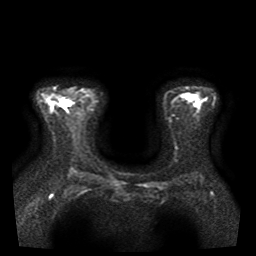
Breast MRI, one axial slice. Position 29 of 41 along the scan axis. Diffusion-weighted series; image 2 of 4 stored at this slice position (different b-values; order by instance number). 1.5 T. 5 mm slice thickness. 256 × 256 image matrix, field of view 330 × 330 mm. Female patient.
Outlined on this slice (outlined manually by an expert reader):
- tumour on diffusion-weighted imaging: bounding box (x1, y1, x2, y2) in pixels: (69, 101, 75, 106)